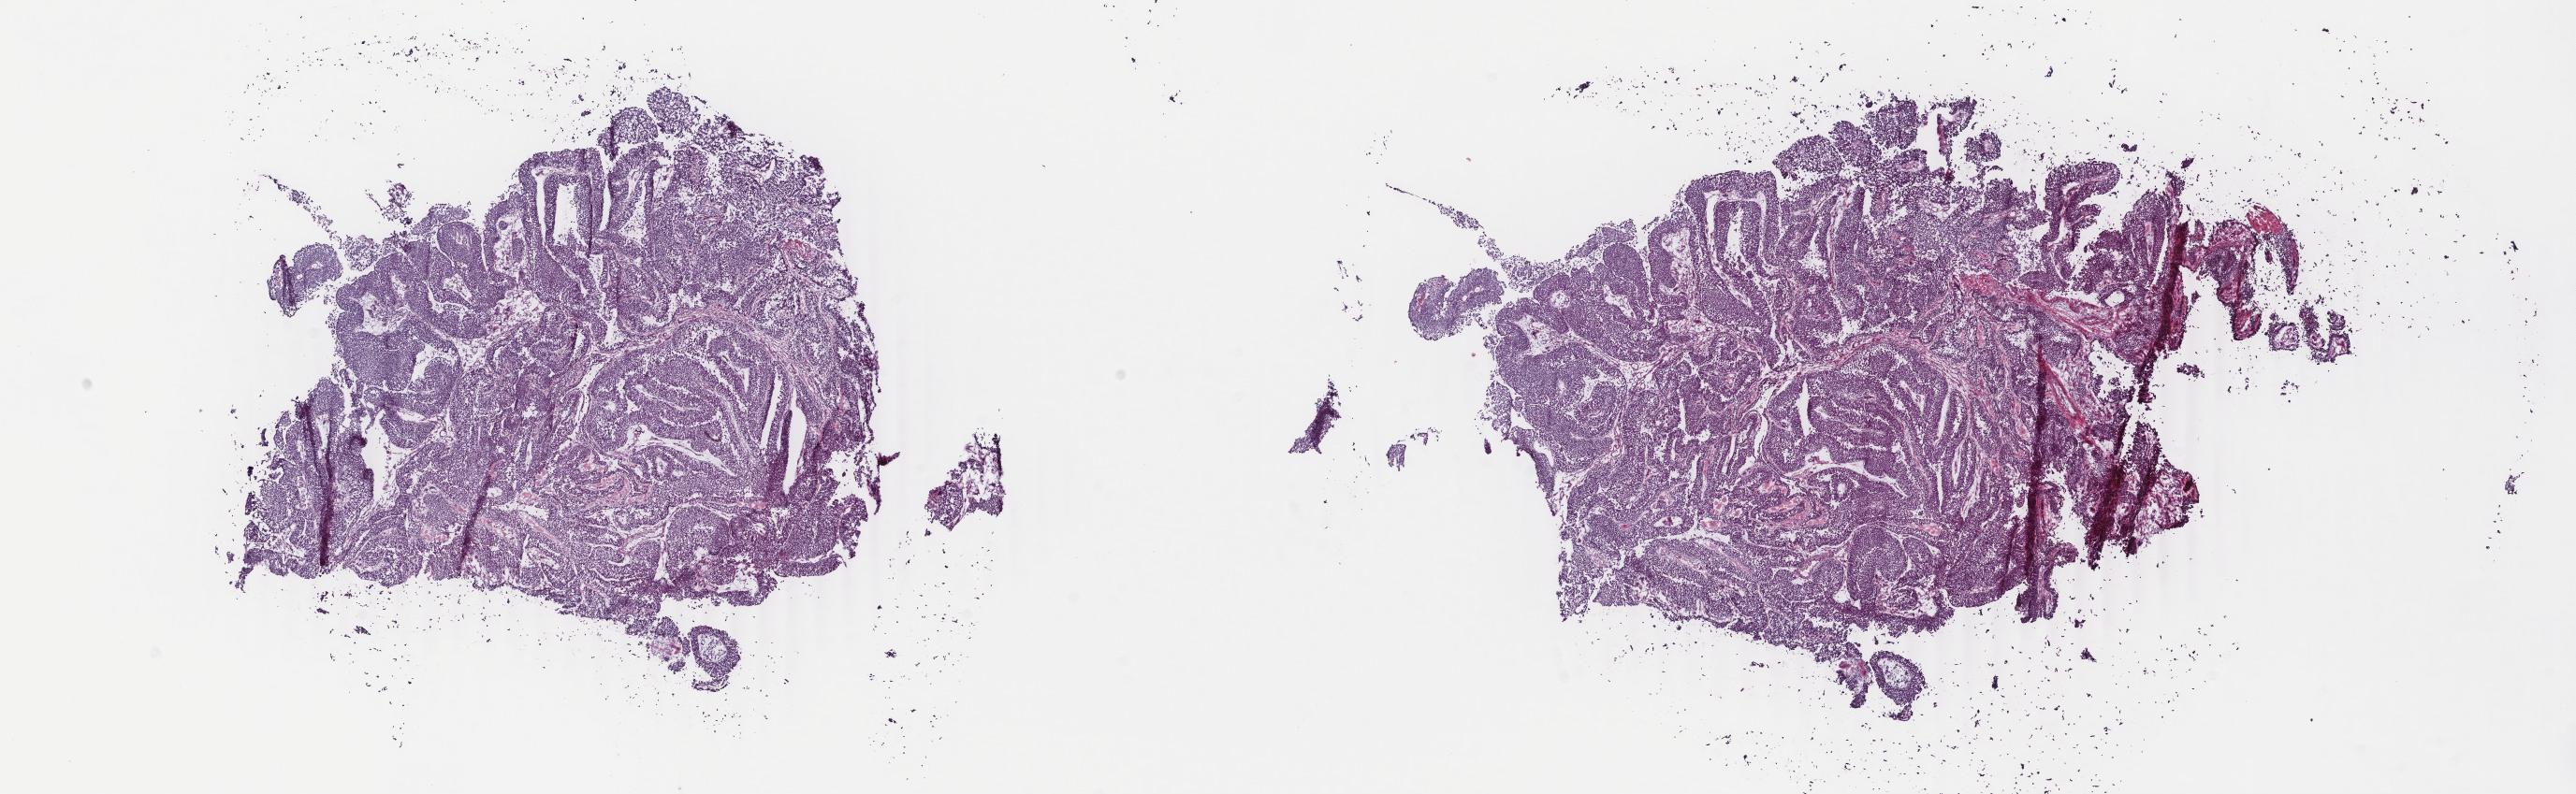
H&E-stained whole-slide image, a low-resolution overview of the entire scanned area, about 21.9 x 6.8 mm (acquisition: 40x scan). Frozen section. Bladder, primary tumour sample. Male patient; age at initial diagnosis 57 years. Histologic grade: high grade. Composition of this section per pathologist review: tumour cells 95%, tumour nuclei 95%, normal cells 0%, stromal cells 5%, necrosis 0%. Inflammatory infiltration, as recorded: lymphocyte infiltration 1%, monocyte infiltration 0%, neutrophil infiltration 0%.
Histologic diagnosis: Transitional cell carcinoma. Lymph nodes positive (case pathology): 0 of 13 examined. AJCC pathologic stage: III (6th edition).